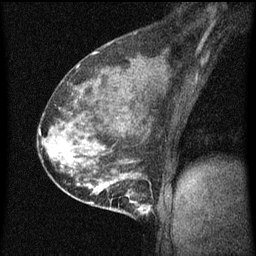
Breast MRI (dynamic contrast-enhanced), one sagittal slice; position 36 of 60 along the scan axis; dynamic contrast-enhanced series, image 2 of 3 at this slice position (ordered by acquisition); 1.5 T; TE 4.2 ms, TR 8 ms; 2 mm slice thickness; 256 × 256 image matrix, field of view 180 × 180 mm. Female patient, age 35 years.
Annotated regions visible in this slice (semi-automatic segmentation, software-assisted and operator-edited):
- analysis volume of interest (the breast-tissue region the enhancement analysis was run in; not a lesion): box from (x=110, y=178) to (x=155, y=219) px
- tumour enhancement mask (voxels above the 70 % enhancement threshold inside the analysis volume of interest): (x=111, y=178)–(x=152, y=215)